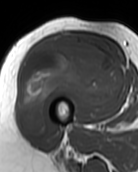
MRI of an extremity soft-tissue mass, one axial slice. Slice 48 of 99 in the series (ordered by position). MR volume resampled by the dataset authors to the PET/CT grid (not the native acquisition matrix). 138 × 172 image matrix. Female patient. From the clinical record (not read from this slice): histological type: pleiomorphic undifferentiated sarcoma; grade: high; site of the primary tumour: right quadricep.
Structures marked on this image (expert contour drawn on MRI and transferred to this co-registered scan by the dataset authors):
- gross tumour volume including surrounding oedema: box from (x=19, y=34) to (x=122, y=136) px
- gross tumour volume (mass): (x=19, y=34)–(x=122, y=136)